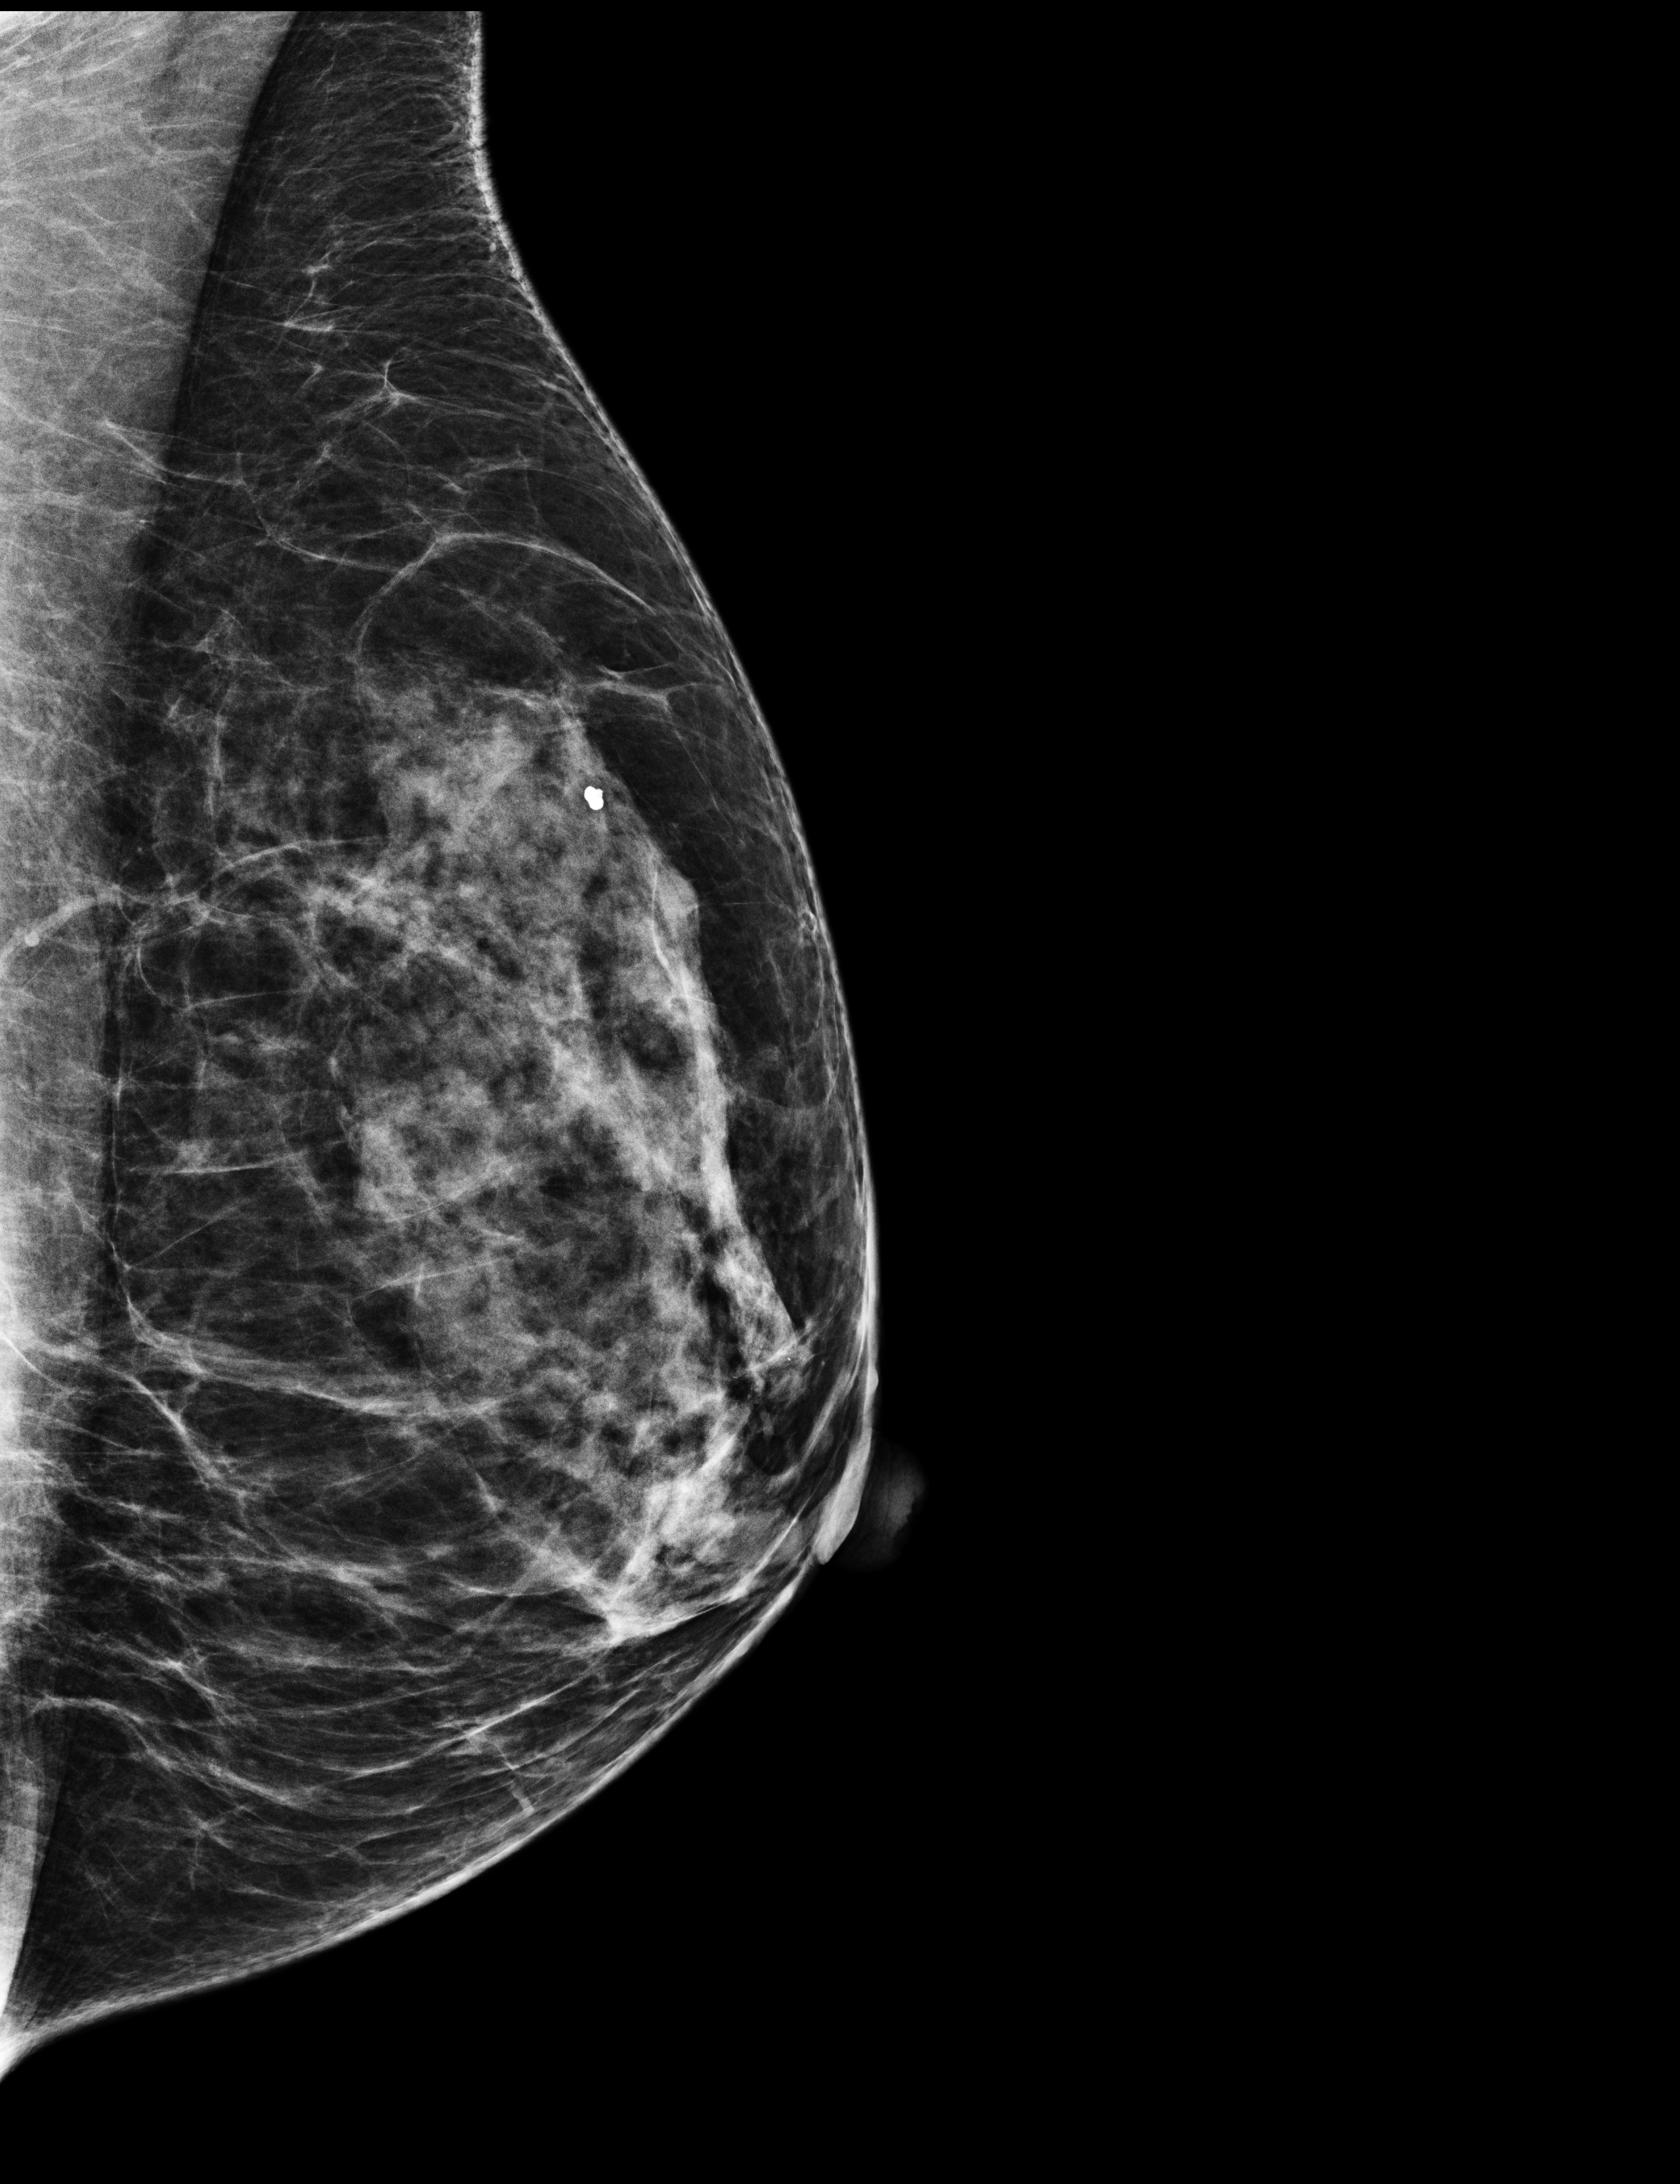
Full-field digital mammogram (FFDM); left breast; MLO view; annual screening mammography examination; compressed breast thickness 45 mm. Female patient, age 60 years.
BI-RADS breast density category at the screening exam (both breasts, scale 1–4): 3.